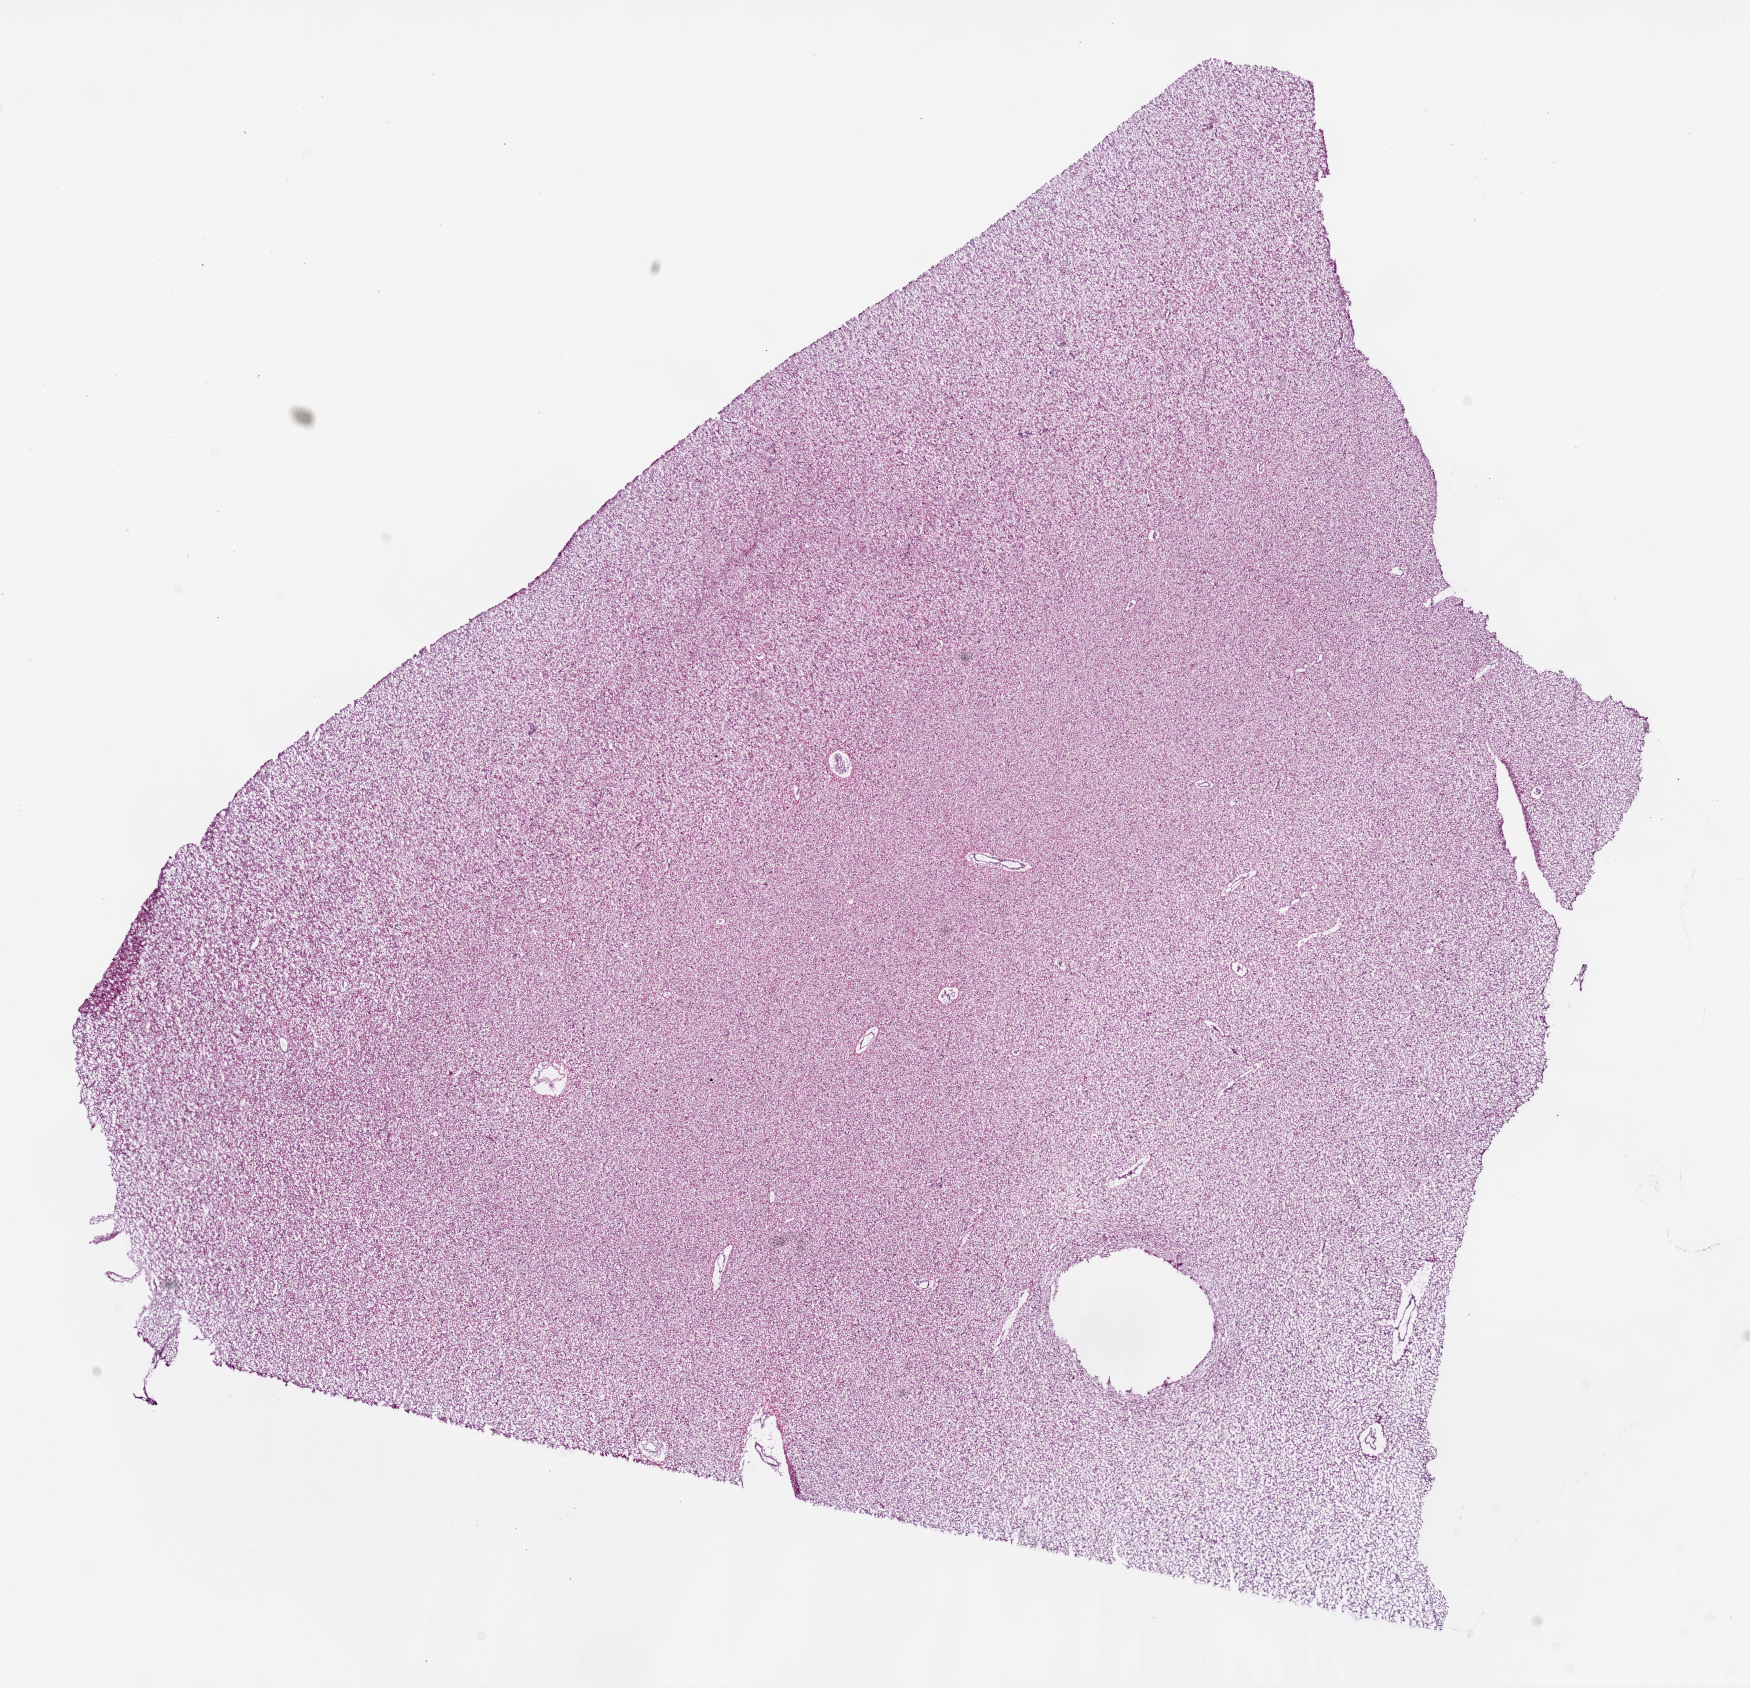
Whole-slide histology image, H&E-stained — shown as a low-resolution overview of the whole scanned area (about 14.0 x 13.5 mm). Frozen section from the top of the tissue portion. Primary tumour sample from the brain. Male patient; age at initial diagnosis 33 years. Histologic grade: G3 (poorly differentiated). Pathologist review of this section (percent, as recorded): tumour cells 100%, tumour nuclei 60%, normal cells 0%, stromal cells 0%, necrosis 0%.
* laterality: right
* diagnosis: Astrocytoma, anaplastic (cerebrum)